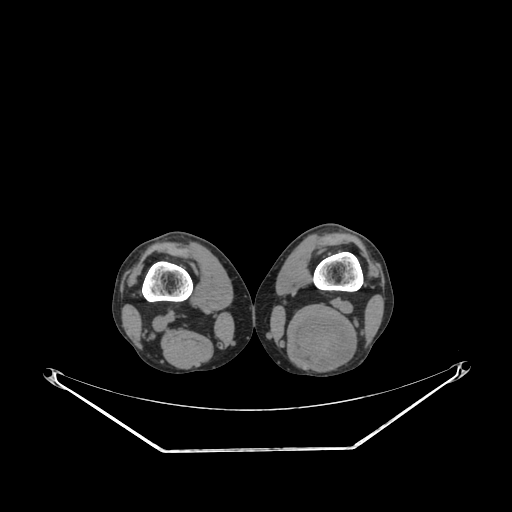
CT of an extremity soft-tissue mass (from a PET/CT study), one axial slice. Slice 192 of 267 in the series (ordered by position). Reconstruction kernel SOFT. Soft-tissue window (W 400 / L 40 HU). 3.75 mm slice thickness. 512 × 512 image matrix, field of view 500 × 500 mm. Male patient. From the clinical record (not read from this slice): histological type: synovial sarcoma; site of the primary tumour: left poplietal fossa.
Annotated regions visible in this slice (expert contour drawn on MRI and transferred to this co-registered scan by the dataset authors):
- gross tumour volume (mass): bounding box (x1, y1, x2, y2) in pixels: (290, 317, 359, 369)